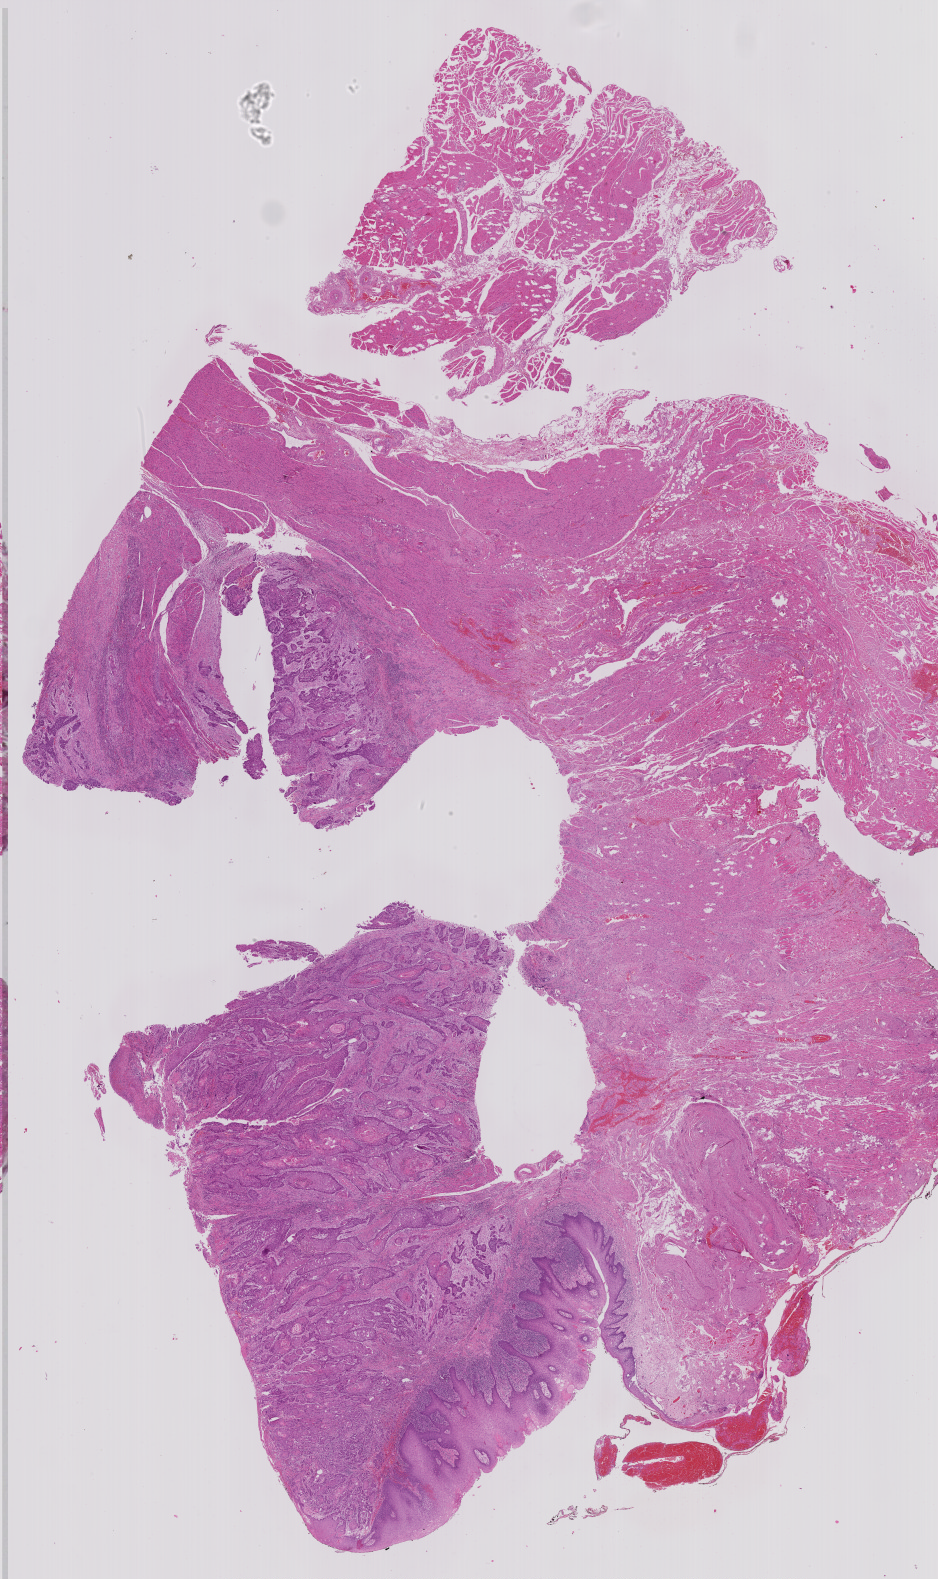
Whole-slide histology image, H&E — a low-resolution overview of the entire scanned area, about 15.0 x 25.3 mm; FFPE section; primary tumour sample from the head and neck. Patient: male, age at initial diagnosis 58 years. Histologic grade: G2 (moderately differentiated).
Diagnosis: Squamous cell carcinoma, keratinizing, NOS (floor of mouth, NOS).